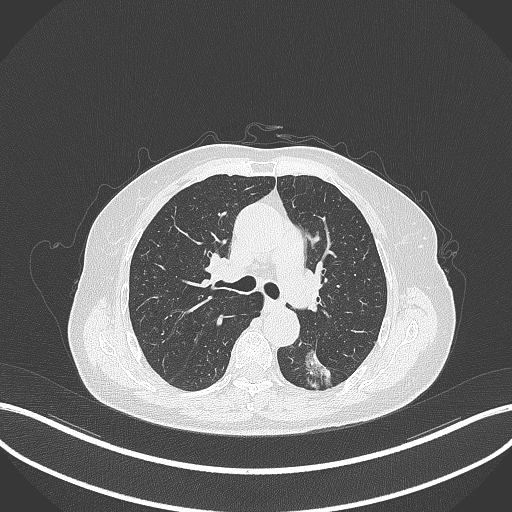
Chest CT, one axial slice; slice 192 of 352 in the series (ordered by position); reconstruction kernel B70f; 120 kVp; lung window (W 1500 / L -600 HU); 1 mm slice thickness; 512 × 512 image matrix, field of view 400 × 400 mm. Female patient, age 70 years. From the clinical record (not read from this slice): clinical TNM (as recorded): T1c N0 M0.
Annotated regions visible in this slice (rectangle marked by the reading radiologist):
- lung tumour (recorded histology: adenocarcinoma): bounding box (x1, y1, x2, y2) in pixels: (301, 342, 336, 394)